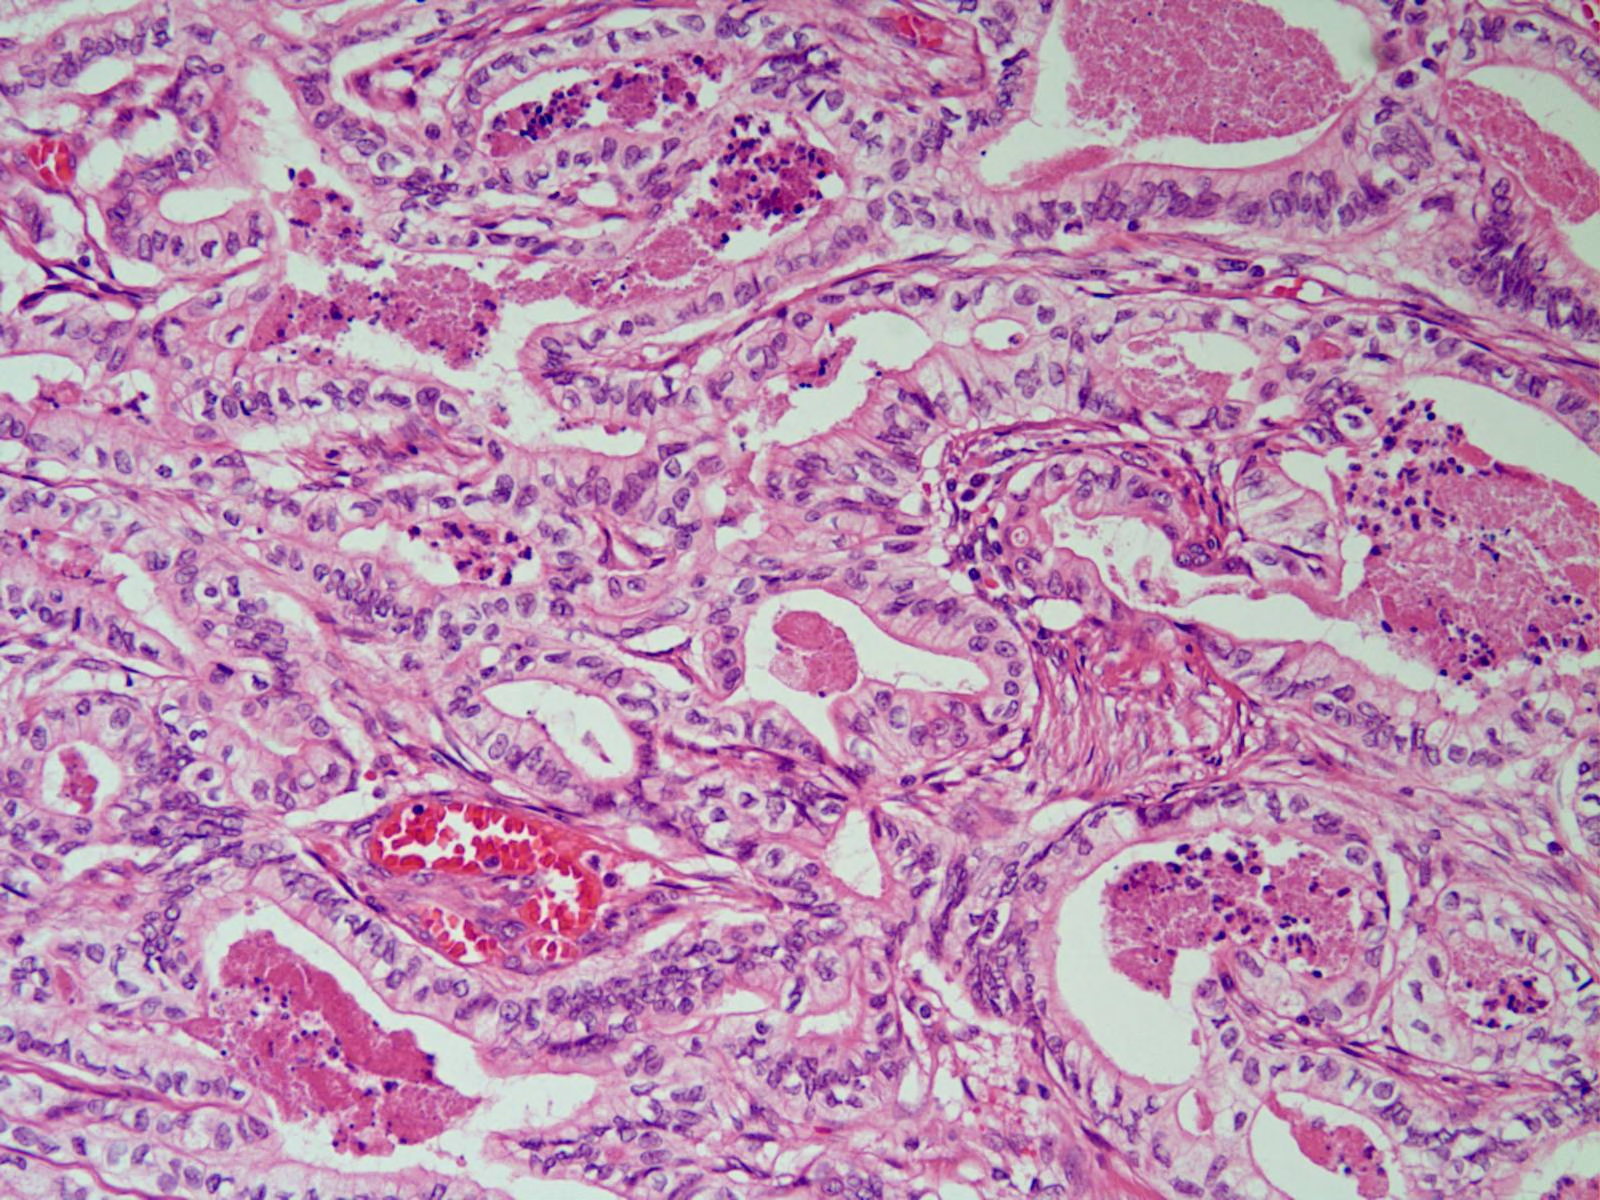
Hematoxylin and eosin (H&E) stained micrograph of a single small tissue field — covering about 0.8 x 0.6 mm, formalin-fixed paraffin-embedded (FFPE) diagnostic section, primary tumour sample from the stomach. Female patient; age at initial diagnosis 74 years. Histologic grade: G2 (moderately differentiated).
Histologic diagnosis: Adenocarcinoma, NOS (gastric antrum).